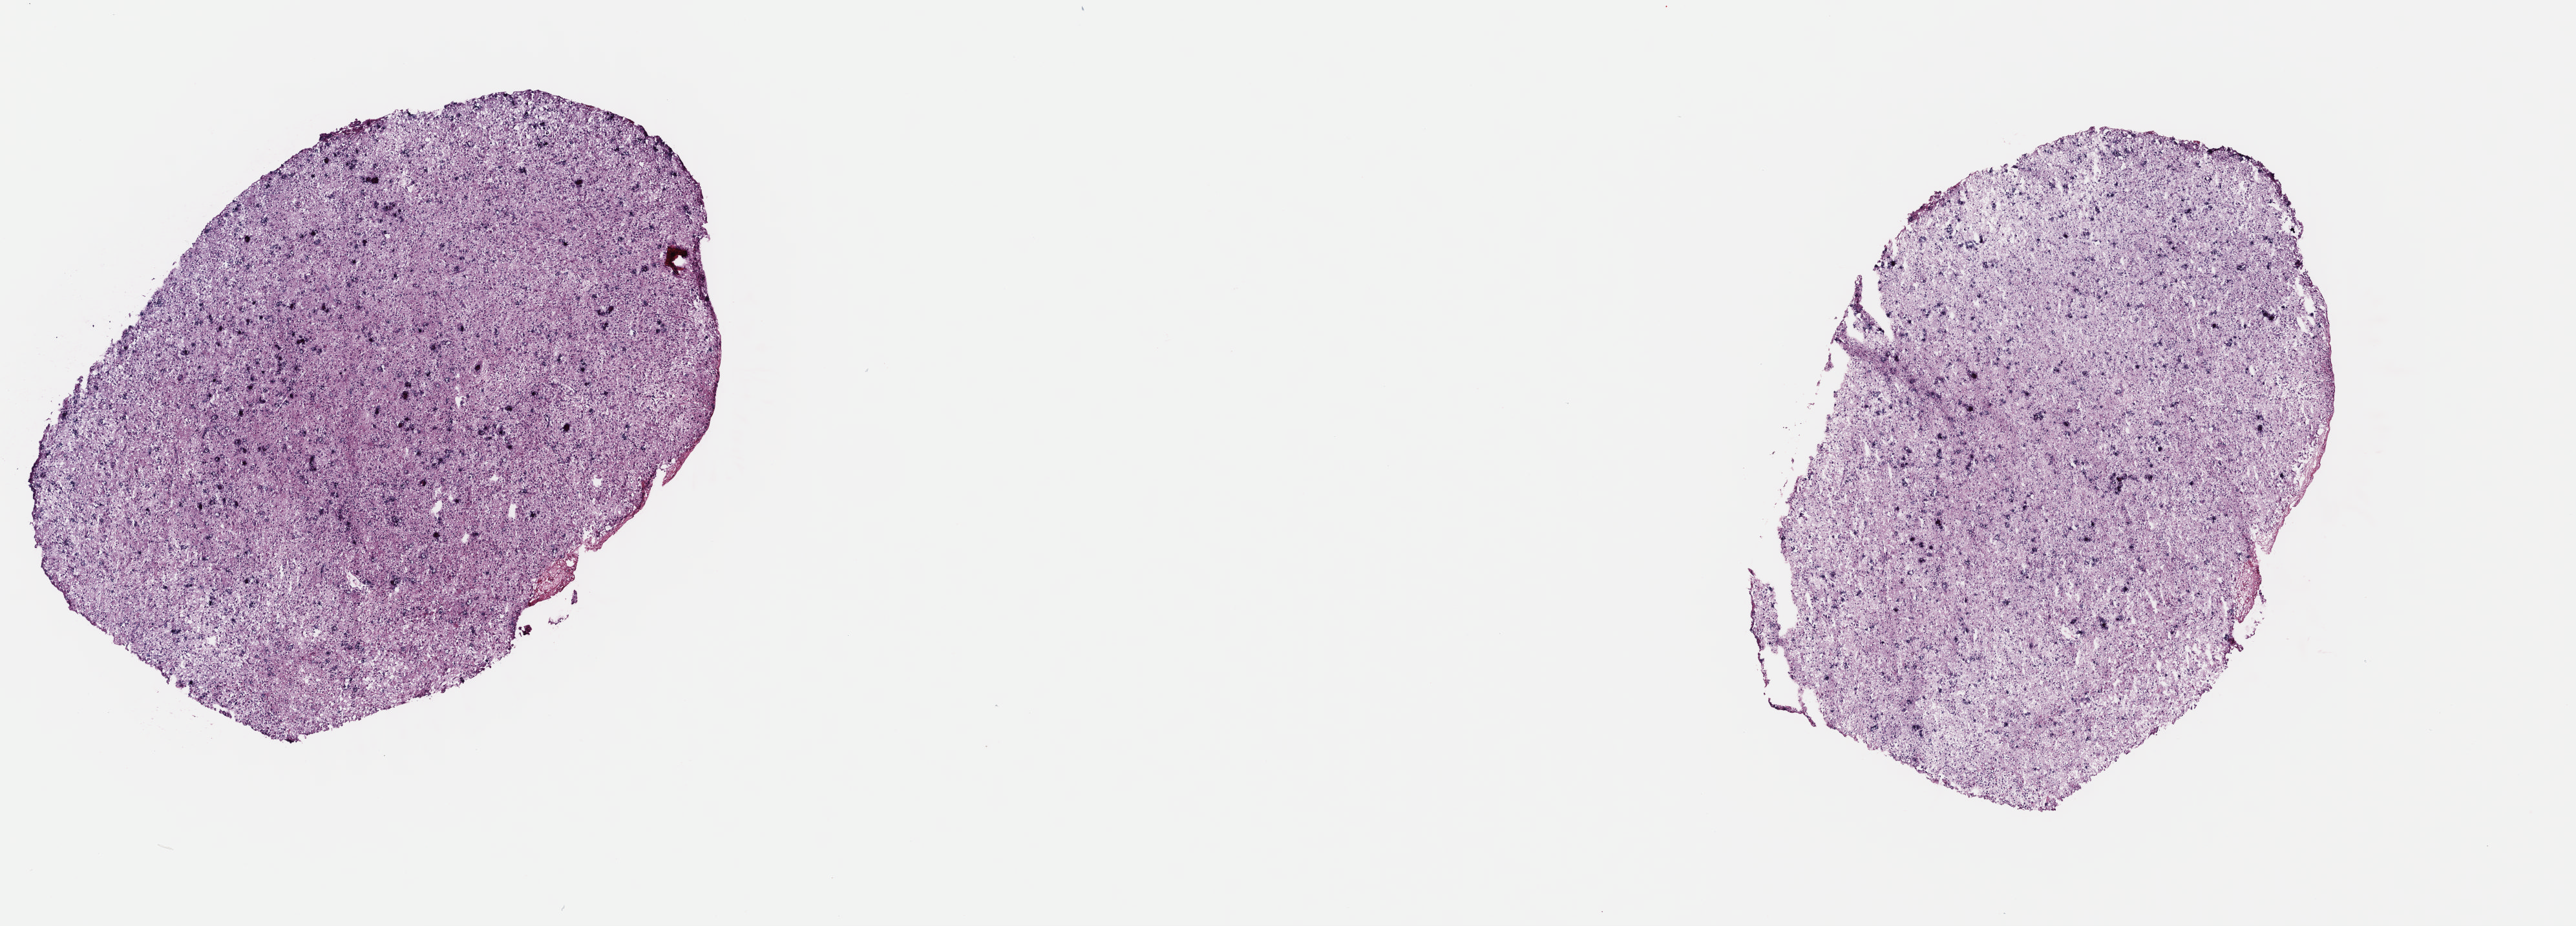
Digitized H&E-stained tissue section (whole slide) — low-resolution overview of the scanned area, about 15.7 x 5.6 mm (acquisition: 40x scan); frozen section from the top of the tissue portion; brain, primary tumour sample. Male patient; age at initial diagnosis 46 years. Histologic grade: G3 (poorly differentiated). Slide review estimates, as recorded: tumour cells 40%, tumour nuclei 90%, normal cells 10%, stromal cells 50%, necrosis 0%. Inflammatory infiltration, as recorded: lymphocyte infiltration 0%, monocyte infiltration 0%, neutrophil infiltration 0%.
Laterality: right. Diagnosis: Astrocytoma, anaplastic (cerebrum).